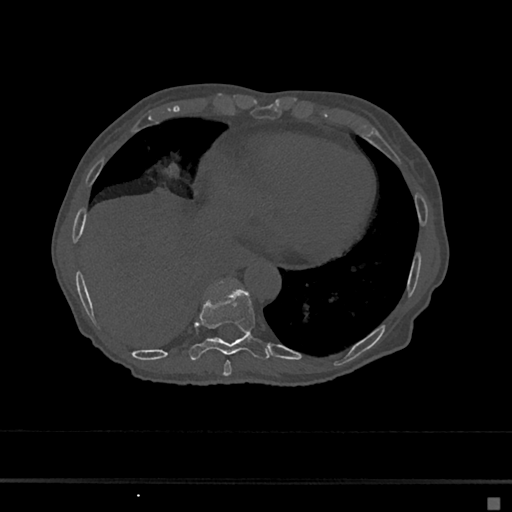
CT including the spine, one axial slice. Slice 272 of 797 in the series (ordered by position). Reconstruction kernel Br40s/3. 120 kVp. Bone window (W 1800 / L 400 HU). 0.5 mm slice thickness. 512 × 512 image matrix, field of view 360 × 360 mm. Patient: female, 68 years. Case-level facts recorded for this patient, not image findings: primary cancer: renal.
Outlined on this slice (semi-automatic segmentation, software-assisted and operator-edited):
- T8 vertebra: bounding box [x1, y1, x2, y2] px = [223, 361, 232, 377]
- T9 vertebra: [188, 287, 272, 361]